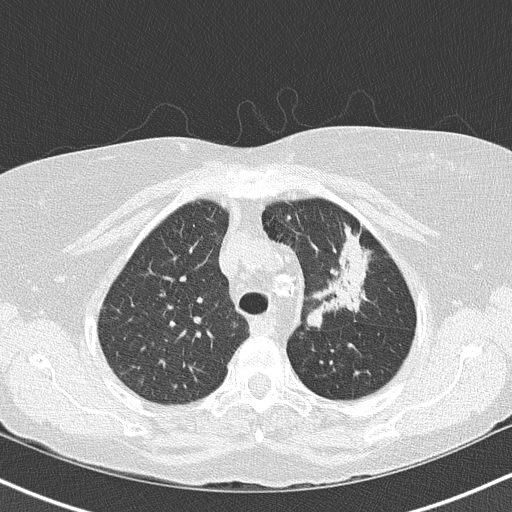
Low-dose screening chest CT, one axial slice; position 116 of 147 along the scan axis; 120 kVp; lung window (W 1500 / L -600 HU); 2 mm slice thickness; 512 × 512 image matrix, field of view 320 × 320 mm.
Outlined on this slice (outlined manually by an expert reader):
- lesion 1 (tumor, upper lobe of left lung): box from (x=330, y=235) to (x=367, y=309) px